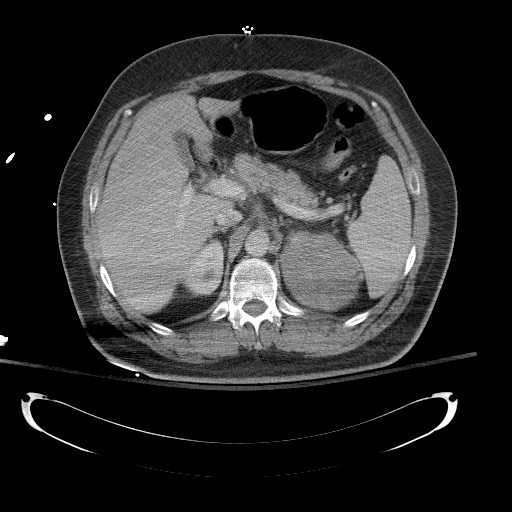
Contrast-enhanced abdominal CT, one axial slice; 120 kVp; intravenous contrast given; soft-tissue window (W 400 / L 40 HU); 512 × 512 image matrix. Patient: male, 43 years. From the clinical record (not read from this slice): diagnosis: adrenocortical carcinoma; tumour side: left adrenal; tumour size at pathology: 9.8 cm; Ki-67 index: 30 %; stage (as recorded): 2.
Outlined on this slice (semi-automatically segmented with operator editing):
- mass: bounding box <281,236,356,309> (left, top, right, bottom; pixels)